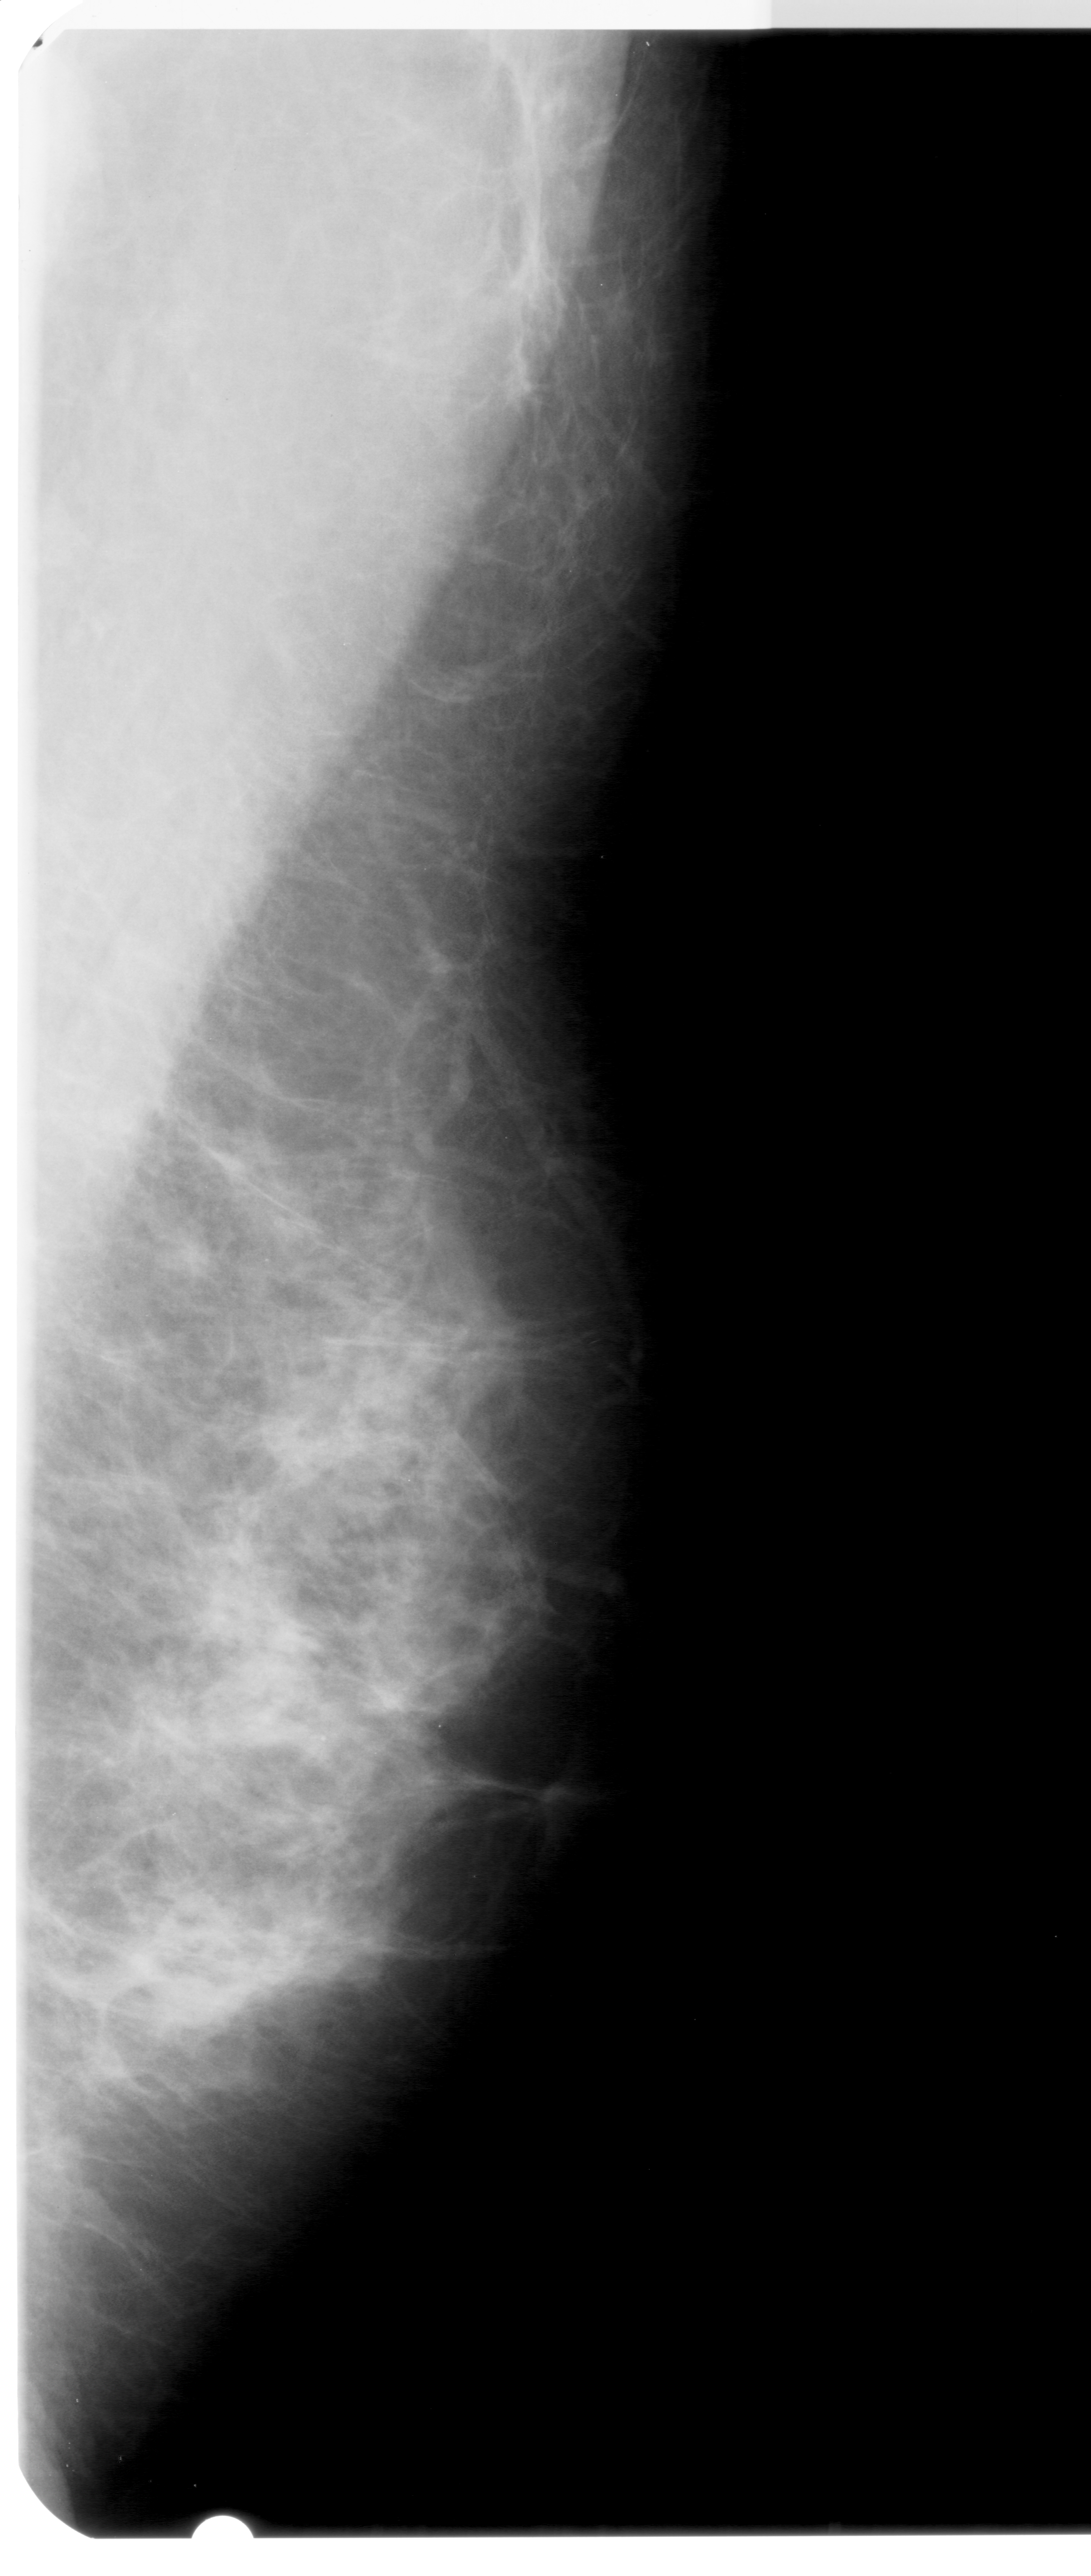
Mammogram (digitized film); right breast; MLO view; BI-RADS breast density category 4 (scale 1–4); 1091 × 2576 image matrix.
Expert-marked regions of interest on this image (one box per marked abnormality):
- mass, shape architectural distortion, margins ill defined; BI-RADS assessment category 4; subtlety rating 1 on a 1 (subtle) to 5 (obvious) scale; pathology (as recorded): benign: bounding box (x1, y1, x2, y2) in pixels: (202, 1600, 329, 1763)